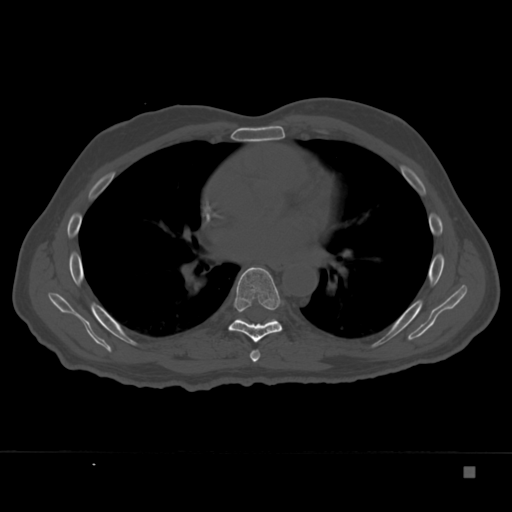
CT including the spine, one axial slice. Position 223 of 332 along the scan axis. Bone window (W 1800 / L 400 HU). 1.5 mm slice thickness. 512 × 512 image matrix, field of view 389 × 389 mm. Male patient, age 72 years. From the clinical record (not read from this slice): primary cancer: skeletal.
Structures marked on this image (semi-automatically segmented with operator editing):
- T6 vertebra: bounding box (x1, y1, x2, y2) in pixels: (250, 350, 261, 362)
- T7 vertebra: (228, 267, 283, 343)